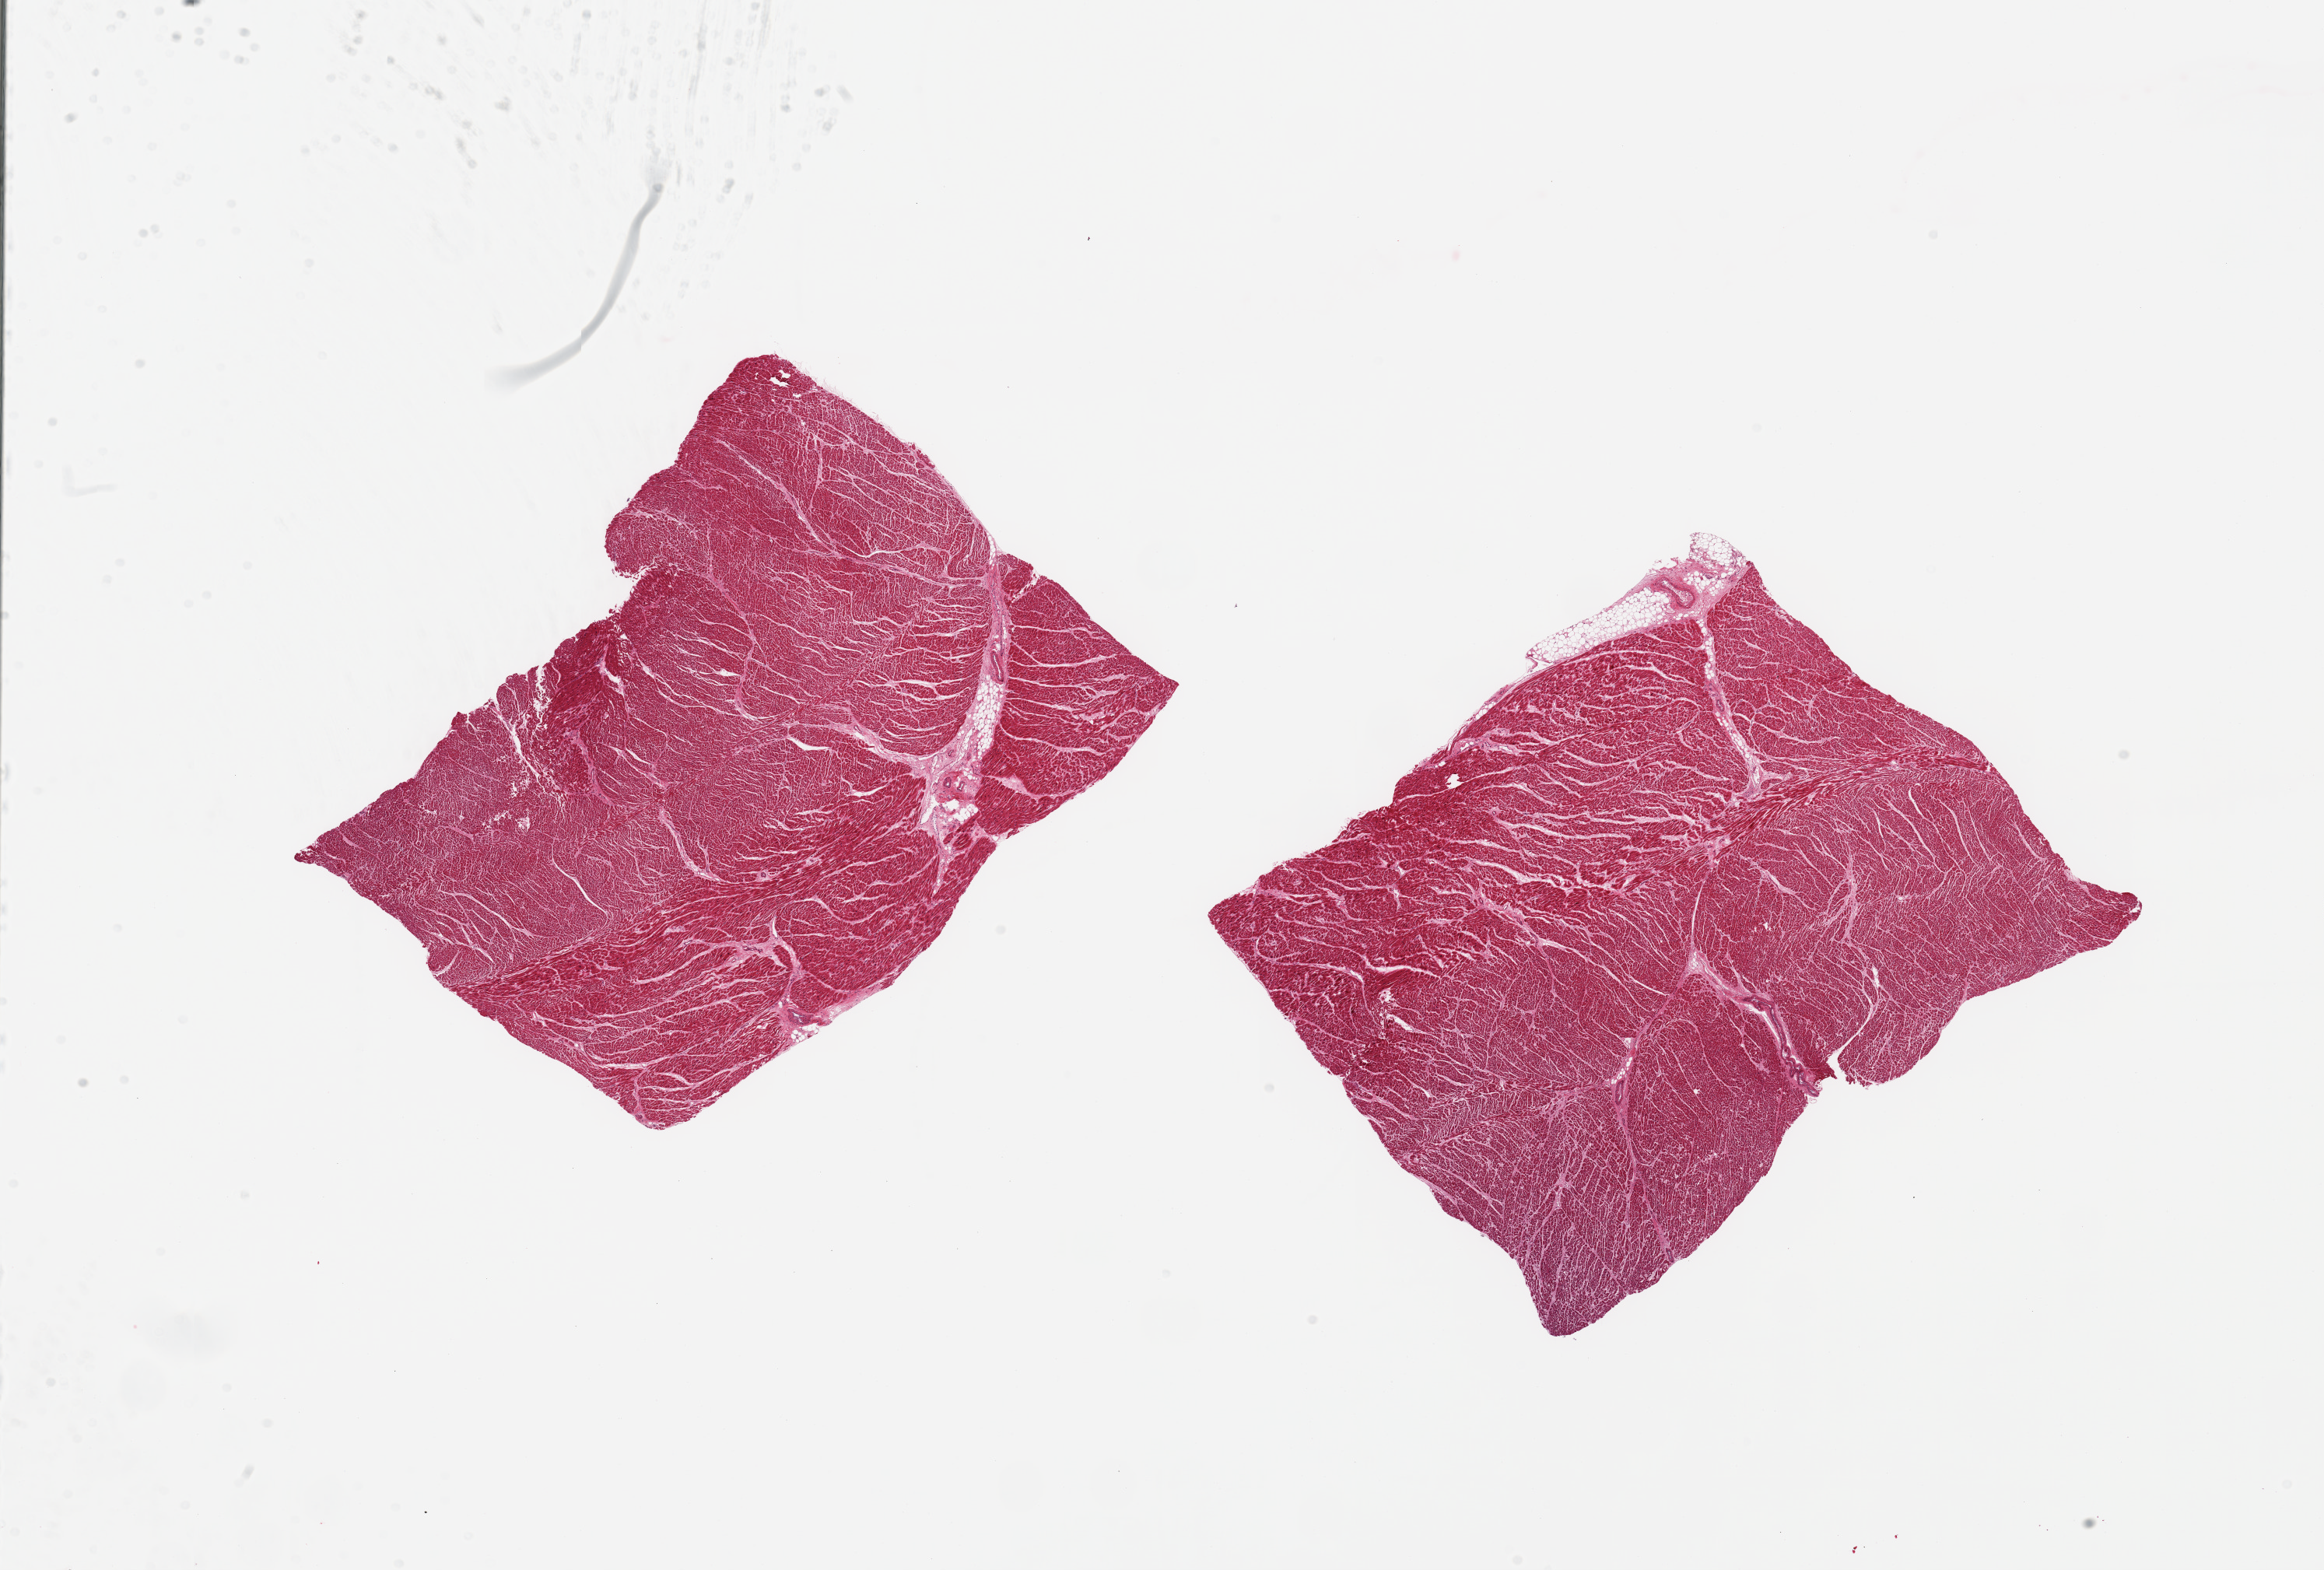
Hematoxylin and eosin (H&E) whole-slide image, whole scanned area (about 23.6 x 16.0 mm, acquisition: 20x scan) shown as a low-resolution overview; PAXgene-fixed paraffin-embedded (PFPE) section; section of heart (target tissue); tissue donor sample.
- reviewer comment on this tissue sample: 2 pieces; <5% fat; no lesions